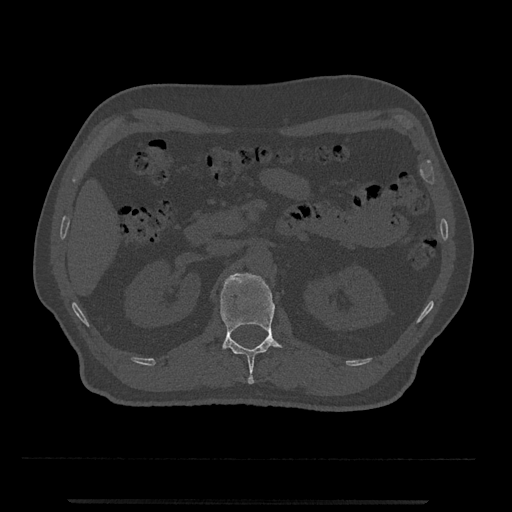
CT including the spine, one axial slice; slice 329 of 797 in the series (ordered by position); reconstruction kernel Br40s/3; bone window (W 1800 / L 400 HU); 0.5 mm slice thickness; 512 × 512 image matrix, field of view 419 × 419 mm. Male patient, age 63 years. Case-level facts recorded for this patient, not image findings: primary cancer: prostate.
Outlined on this slice (semi-automatically segmented with operator editing):
- L1 vertebra: bounding box [x1, y1, x2, y2] px = [220, 273, 289, 384]